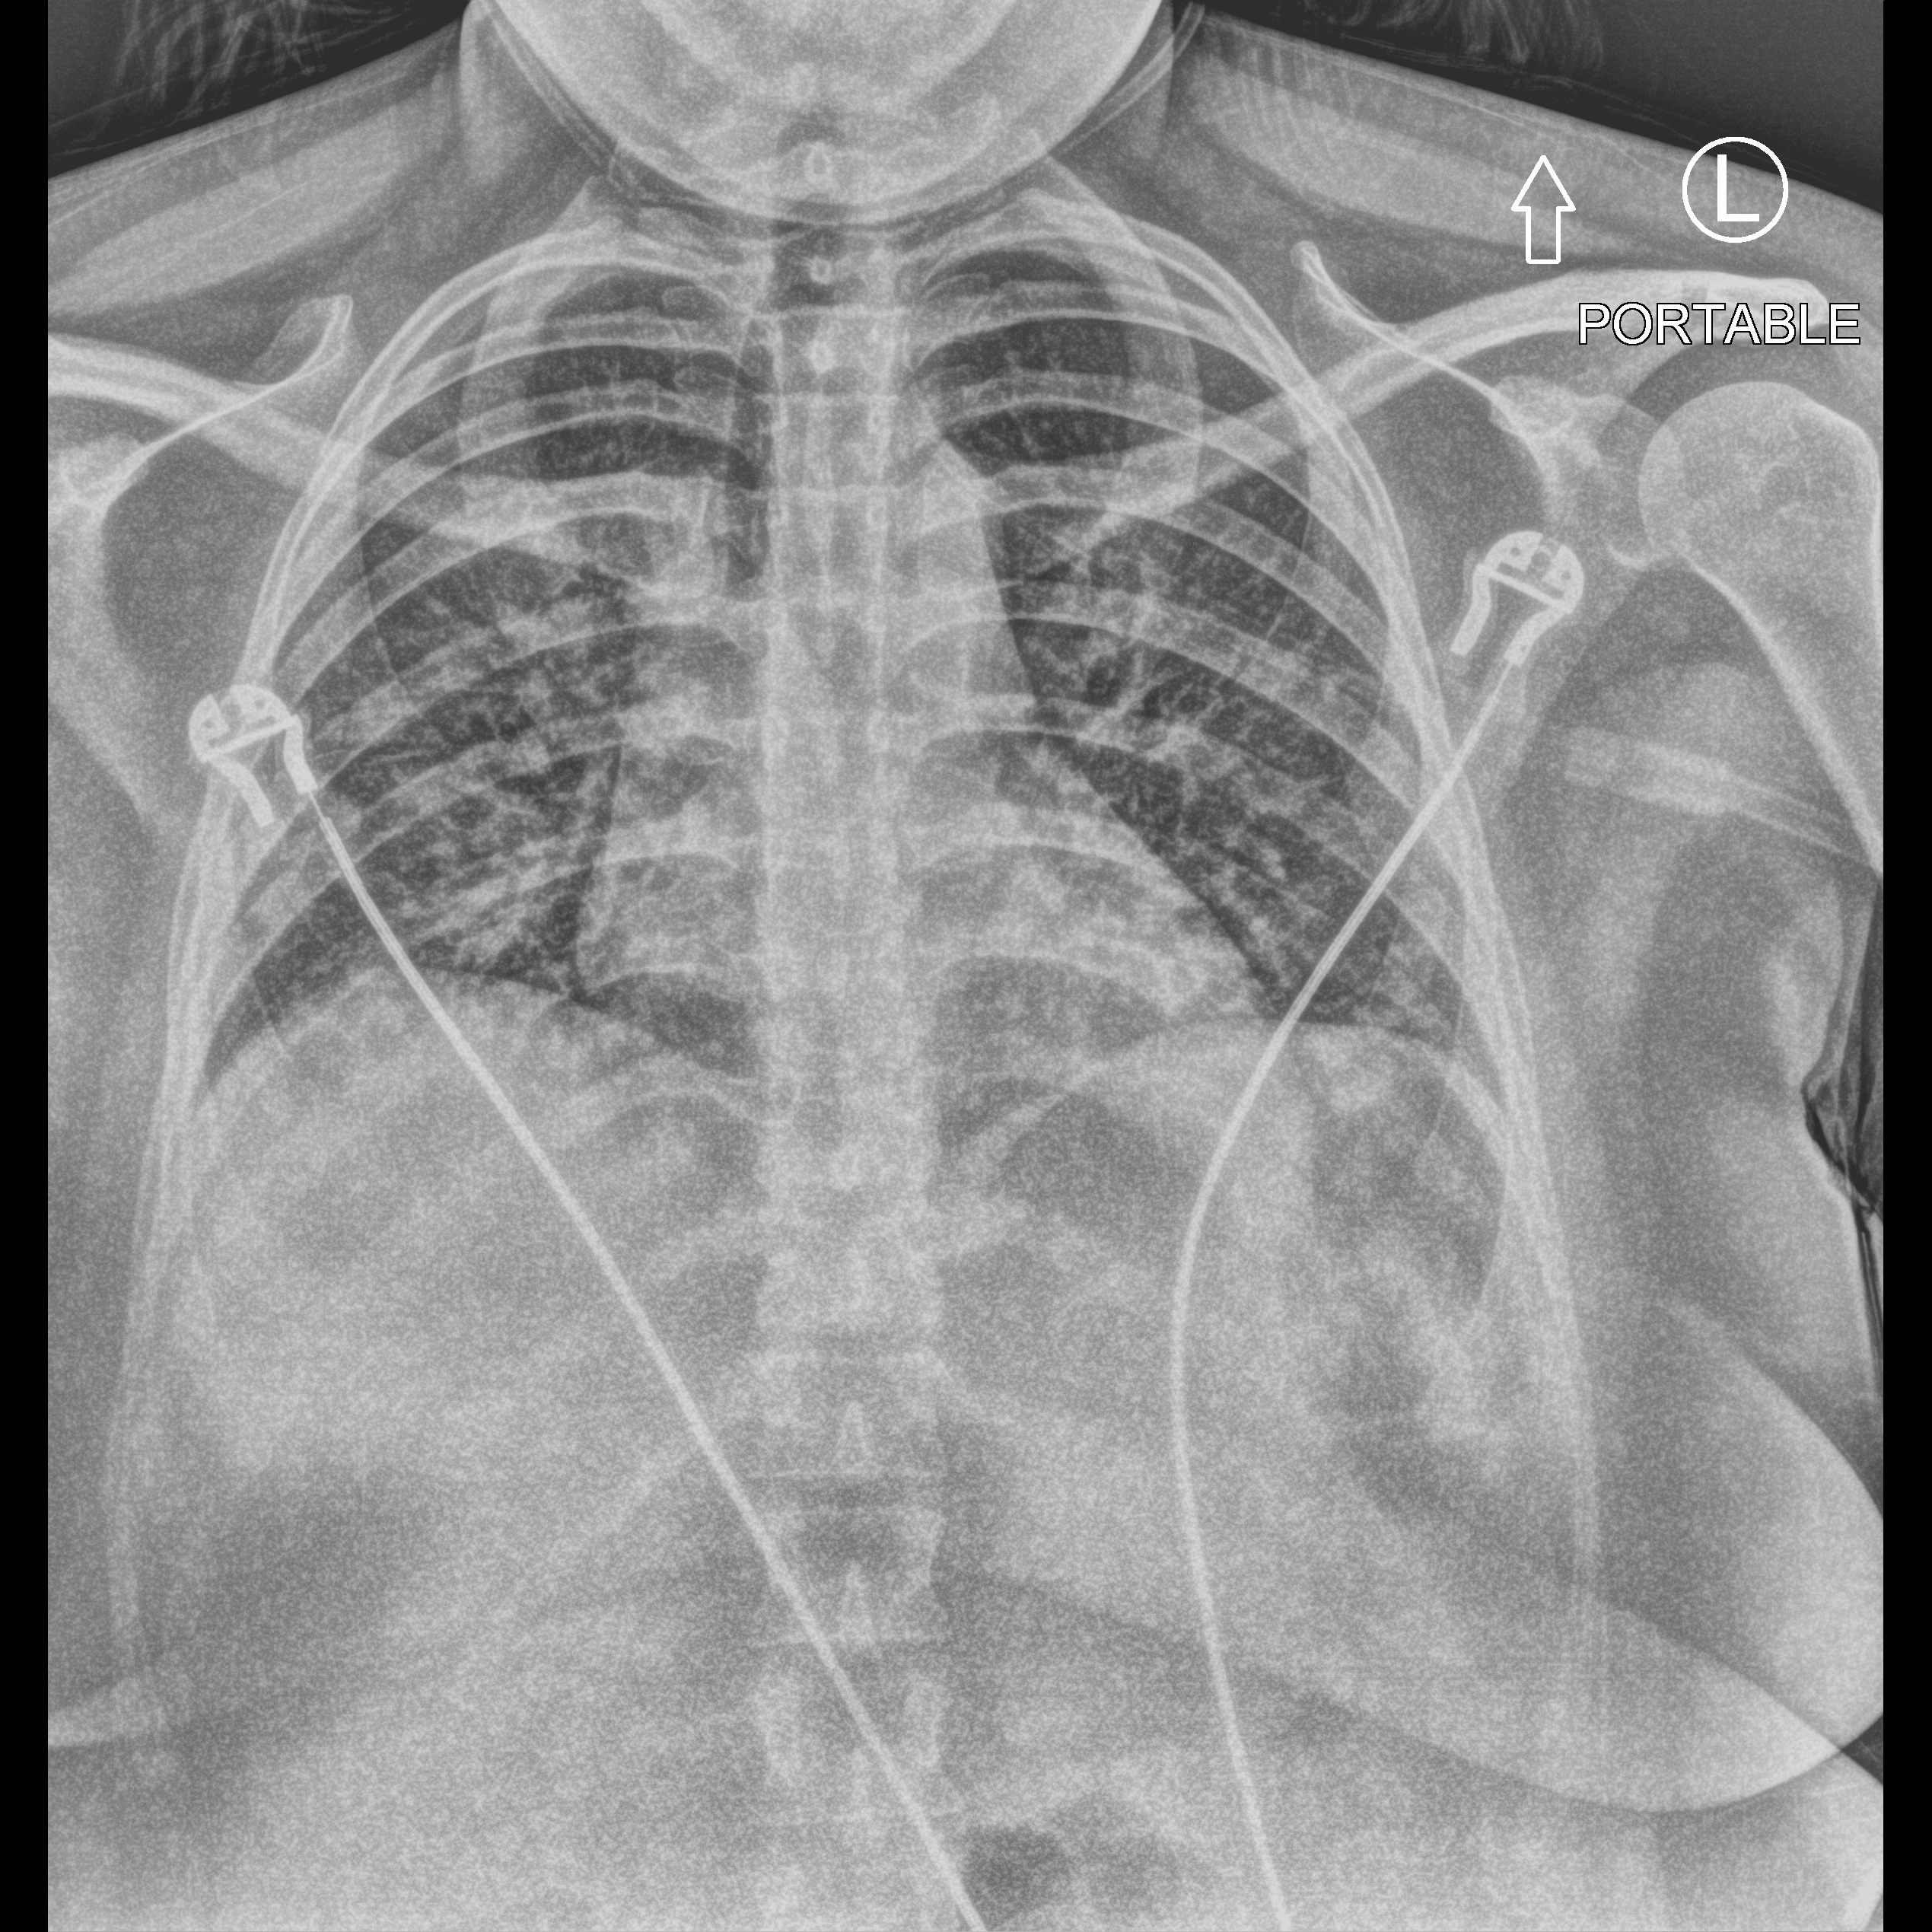
Portable chest radiograph; anteroposterior (AP) projection. Female patient hospitalised with COVID-19, age 18–59 years.
From the hospital-stay record, not from the radiograph (when in the stay this image was taken is not recorded):
- mechanically ventilated during this hospital stay: no
- hypertension (admission record): no
- other chronic lung disease (admission record): yes